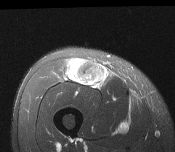
MRI of an extremity soft-tissue mass, one axial slice; position 59 of 116 along the scan axis; T2-weighted fat-saturated; MR volume resampled by the dataset authors to the PET/CT grid (not the native acquisition matrix); 3.27 mm slice thickness; 175 × 152 image matrix, field of view 171 × 148 mm. Male patient. From the clinical record (not read from this slice): histological type: pleiomorphic leiomyosarcoma; grade: intermediate; site of the primary tumour: right thigh.
Outlined on this slice (expert contour drawn on MRI and transferred to this co-registered scan by the dataset authors):
- gross tumour volume including surrounding oedema: bounding box <67,58,107,87> (left, top, right, bottom; pixels)